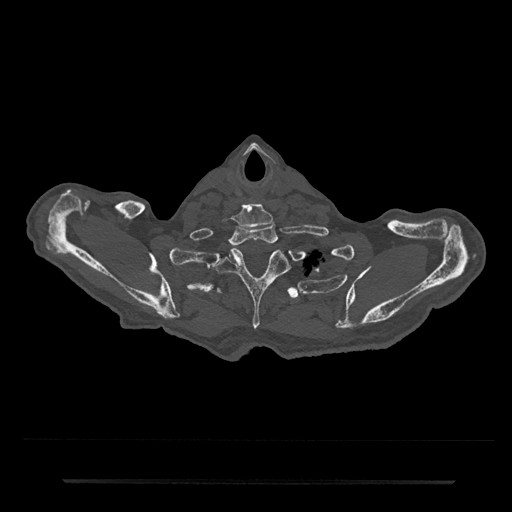
CT including the spine, one axial slice. Slice 703 of 797 in the series (ordered by position). Reconstruction kernel Br40s/3. Bone window (W 1800 / L 400 HU). 0.5 mm slice thickness. 512 × 512 image matrix, field of view 427 × 427 mm. Male patient, age 74 years. From the clinical record (not read from this slice): primary cancer: prostate.
Outlined on this slice (semi-automatically segmented with operator editing):
- T1 vertebra: bounding box <230,224,278,255> (left, top, right, bottom; pixels)
- T2 vertebra: <212,248,289,330>
- T3 vertebra: <216,287,299,301>